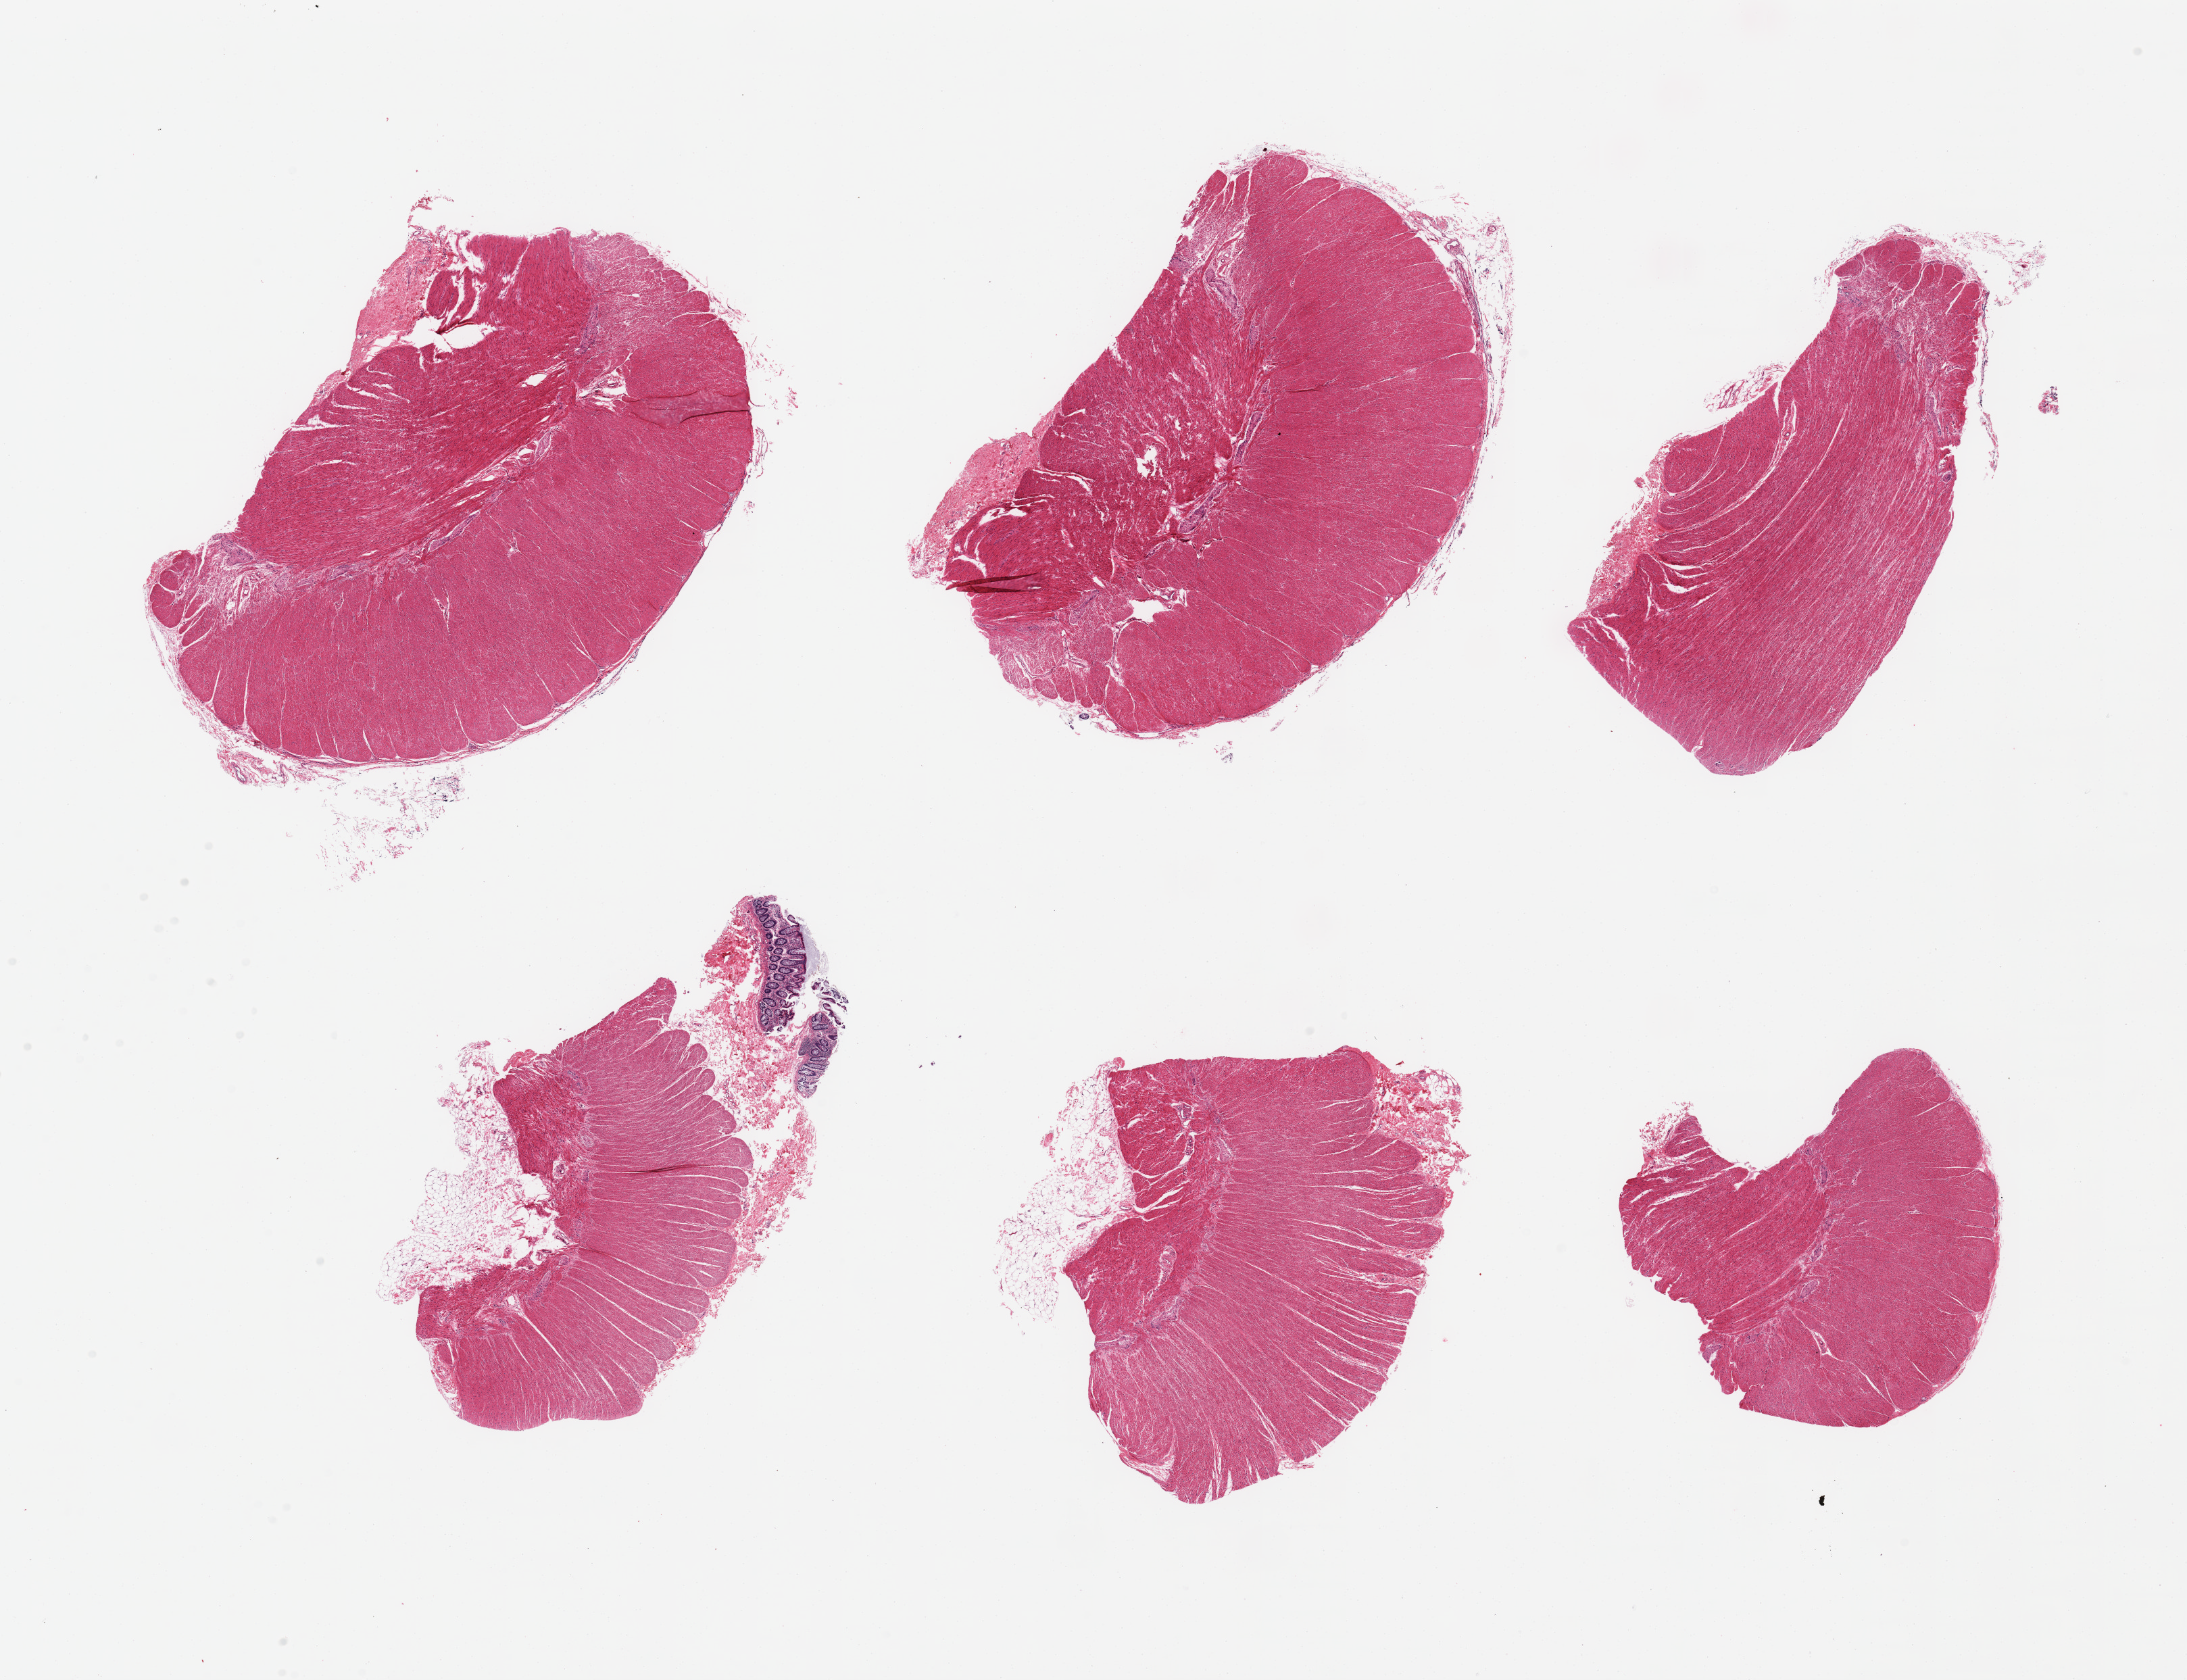
Digitized hematoxylin and eosin (H&E)-stained section — whole scanned area (about 25.6 x 19.7 mm) shown as a low-resolution overview. PAXgene-fixed paraffin-embedded (PFPE) section. Section of sigmoid colon (target tissue). Donor tissue sample.
* review note (as recorded): 6 pieces; target muscularis; small fragment of colonic mucosa